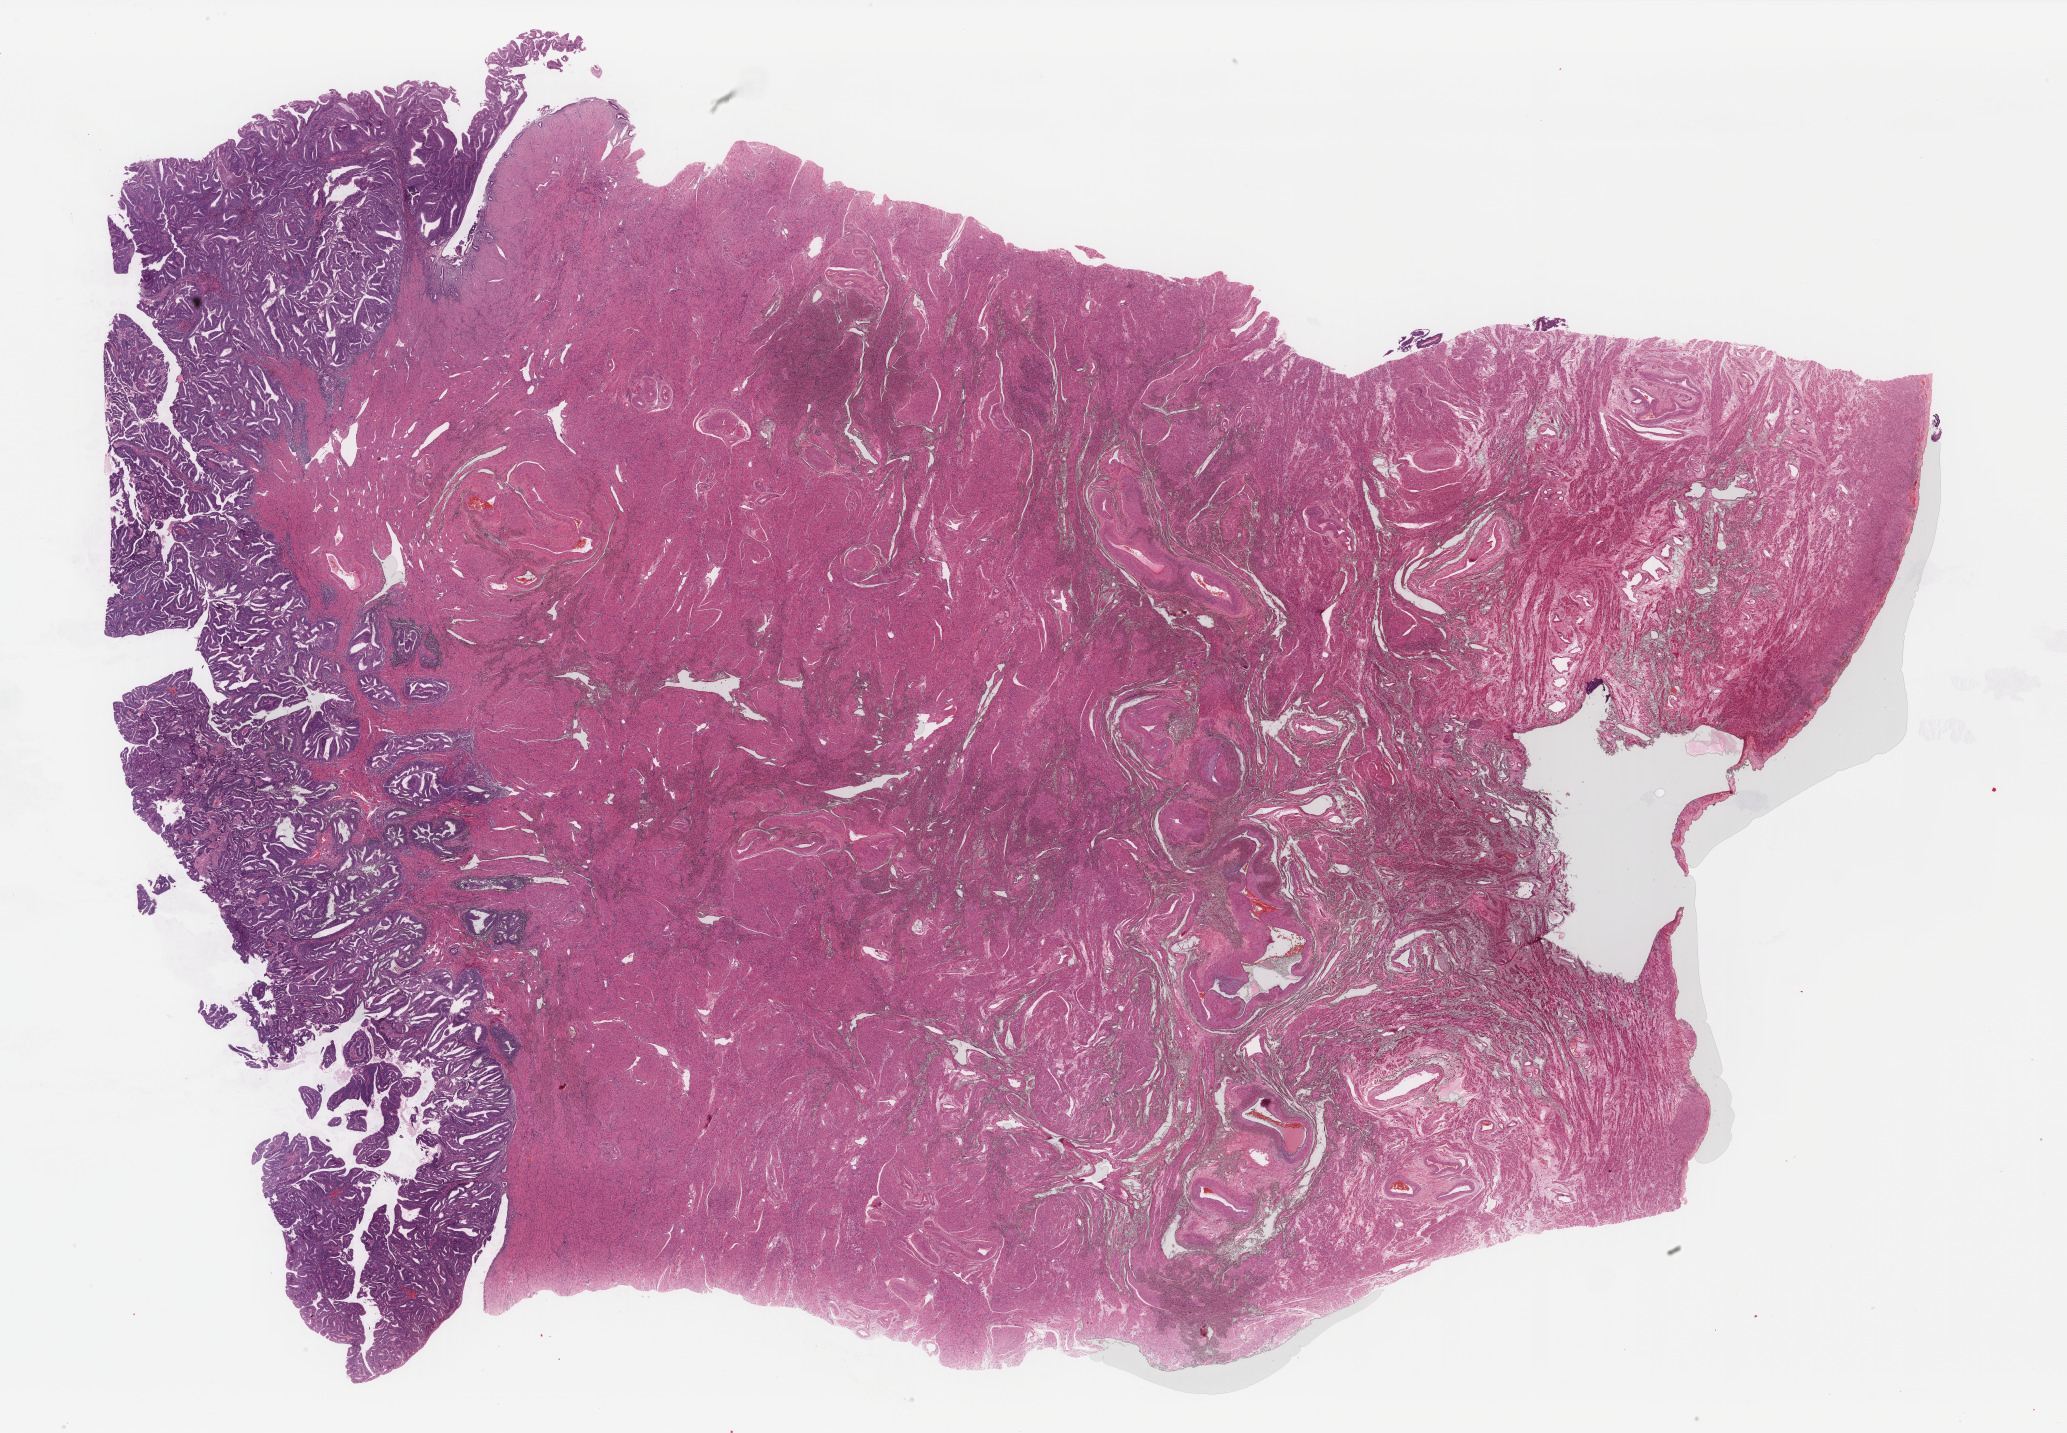
H&E whole-slide image — whole scanned area (about 32.8 x 22.8 mm) shown as a low-resolution overview. FFPE section. Sample: primary tumour, uterus. Female patient; age at initial diagnosis 63 years. Histologic grade: G2 (moderately differentiated).
* lymph nodes positive (case pathology): 0 of 6 examined
* FIGO stage: IA
* diagnosis: Endometrioid adenocarcinoma, NOS (endometrium)